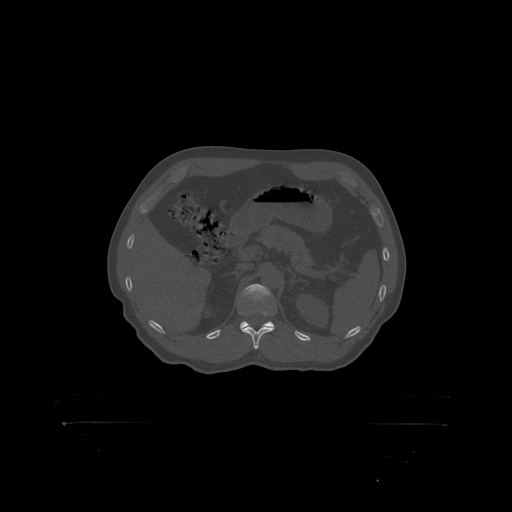
CT including the spine, one axial slice; position 341 of 399 along the scan axis; reconstruction kernel STANDARD; bone window (W 1800 / L 400 HU); 1.25 mm slice thickness; 512 × 512 image matrix, field of view 650 × 650 mm. Patient: male, 46 years. Case-level facts recorded for this patient, not image findings: primary cancer: skin.
Outlined on this slice (semi-automatically segmented with operator editing):
- L1 vertebra: bounding box (x1, y1, x2, y2) in pixels: (239, 285, 275, 316)